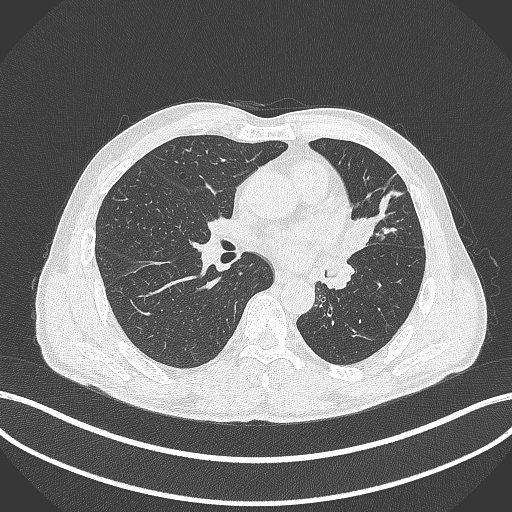
Chest CT, one axial slice. Slice 220 of 429 in the series (ordered by position). Reconstruction kernel B70f. 120 kVp. Lung window (W 1500 / L -600 HU). 1 mm slice thickness. 512 × 512 image matrix, field of view 400 × 400 mm. Patient: male, 57 years. Case-level facts recorded for this patient, not image findings: clinical TNM (as recorded): T2b N0 M0.
Annotated regions visible in this slice (rectangle marked by the reading radiologist):
- lung tumour (recorded histology: squamous cell carcinoma): box from (x=340, y=205) to (x=377, y=262) px